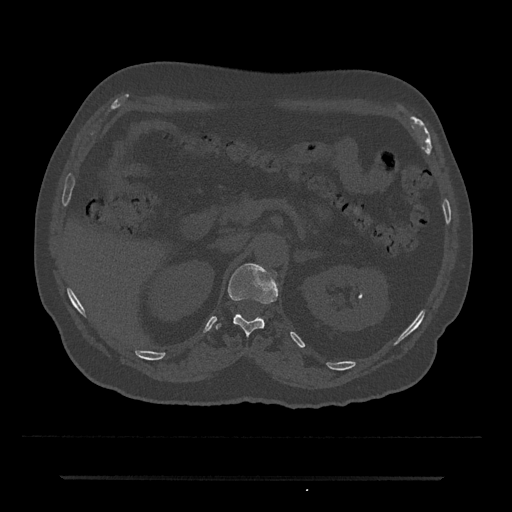
CT including the spine, one axial slice. Position 121 of 797 along the scan axis. Reconstruction kernel Br40s/3. 120 kVp. Bone window (W 1800 / L 400 HU). 0.5 mm slice thickness. 512 × 512 image matrix. Patient: male, 69 years. Case-level facts recorded for this patient, not image findings: primary cancer: prostate.
Outlined on this slice (semi-automatic segmentation, software-assisted and operator-edited):
- T12 vertebra: bounding box <216,264,278,336> (left, top, right, bottom; pixels)